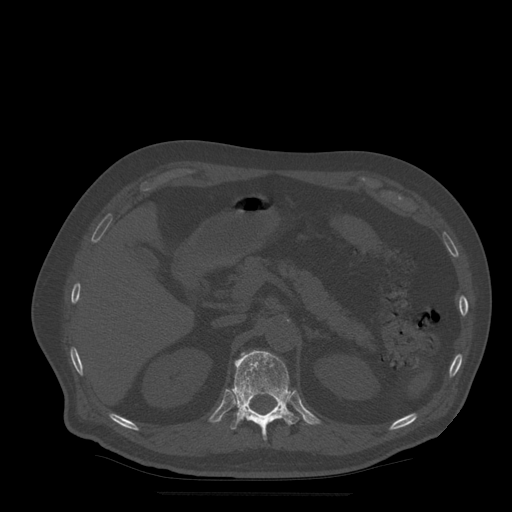
CT including the spine, one axial slice; slice 219 of 522 in the series (ordered by position); bone window (W 1800 / L 400 HU); 1.25 mm slice thickness; 512 × 512 image matrix. Patient age 72 years. From the clinical record (not read from this slice): primary cancer: prostate.
Structures marked on this image (semi-automatically segmented with operator editing):
- T12 vertebra: bounding box [x1, y1, x2, y2] px = [230, 351, 299, 440]